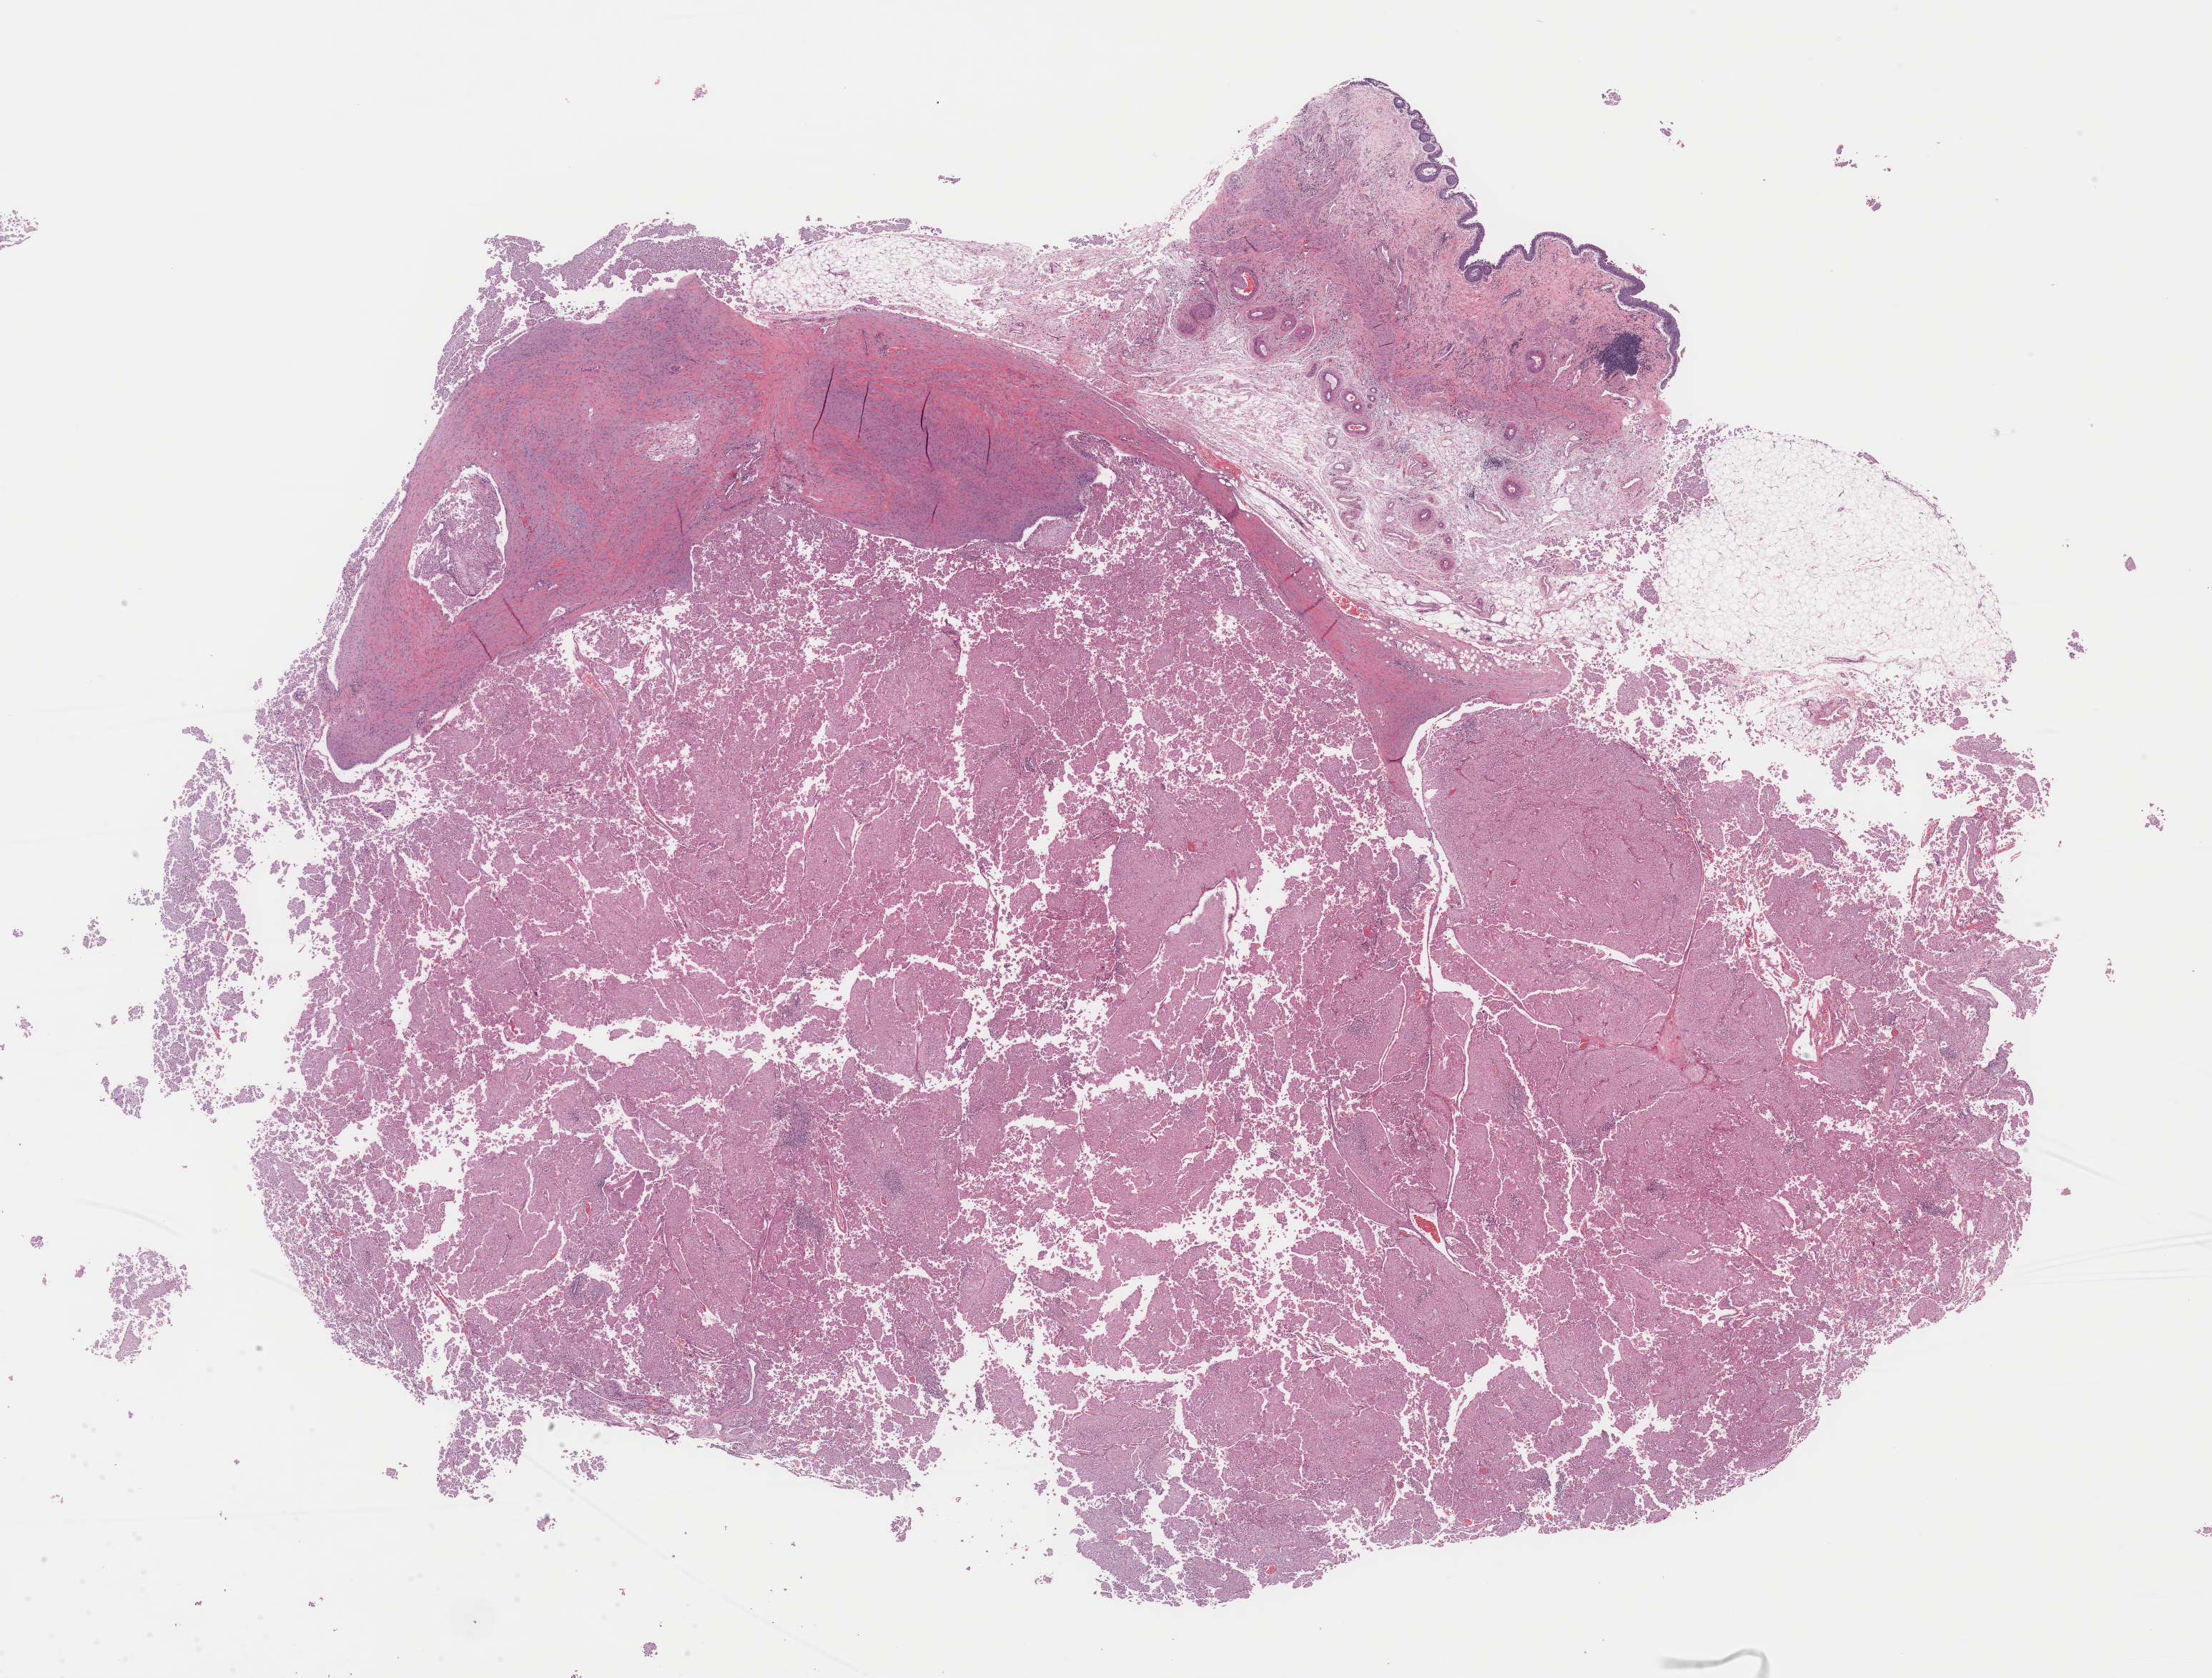
Digitized H&E-stained tissue section (whole slide), shown as a low-resolution overview of the whole scanned area (about 24.4 x 18.5 mm, from a 40x scan); FFPE section; kidney, primary tumour sample. Patient: male, age at initial diagnosis 47 years.
* AJCC pathologic stage: III (7th edition)
* laterality: left
* lymph nodes positive (case pathology): 3 of 3 examined
* diagnosis: Renal cell carcinoma, chromophobe type